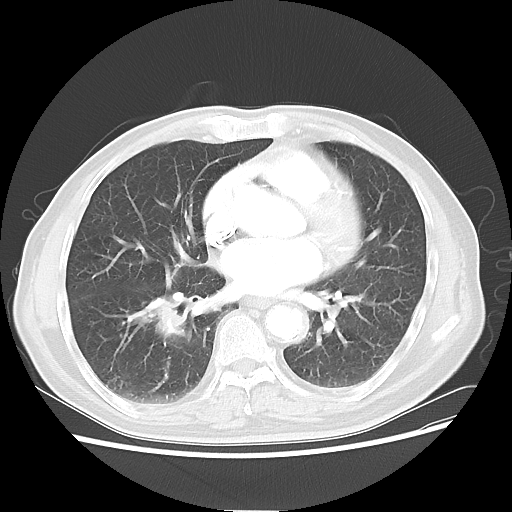
Chest CT, one axial slice. Position 27 of 58 along the scan axis. Reconstruction kernel LUNG. Lung window (W 1500 / L -600 HU). 5 mm slice thickness. 512 × 512 image matrix, field of view 360 × 360 mm. Patient: male, 74 years. Case-level facts recorded for this patient, not image findings: clinical TNM (as recorded): T1c N1 M1.
Annotated regions visible in this slice (rectangle marked by the reading radiologist):
- lung tumour (recorded histology: adenocarcinoma): bounding box [x1, y1, x2, y2] px = [125, 297, 195, 351]